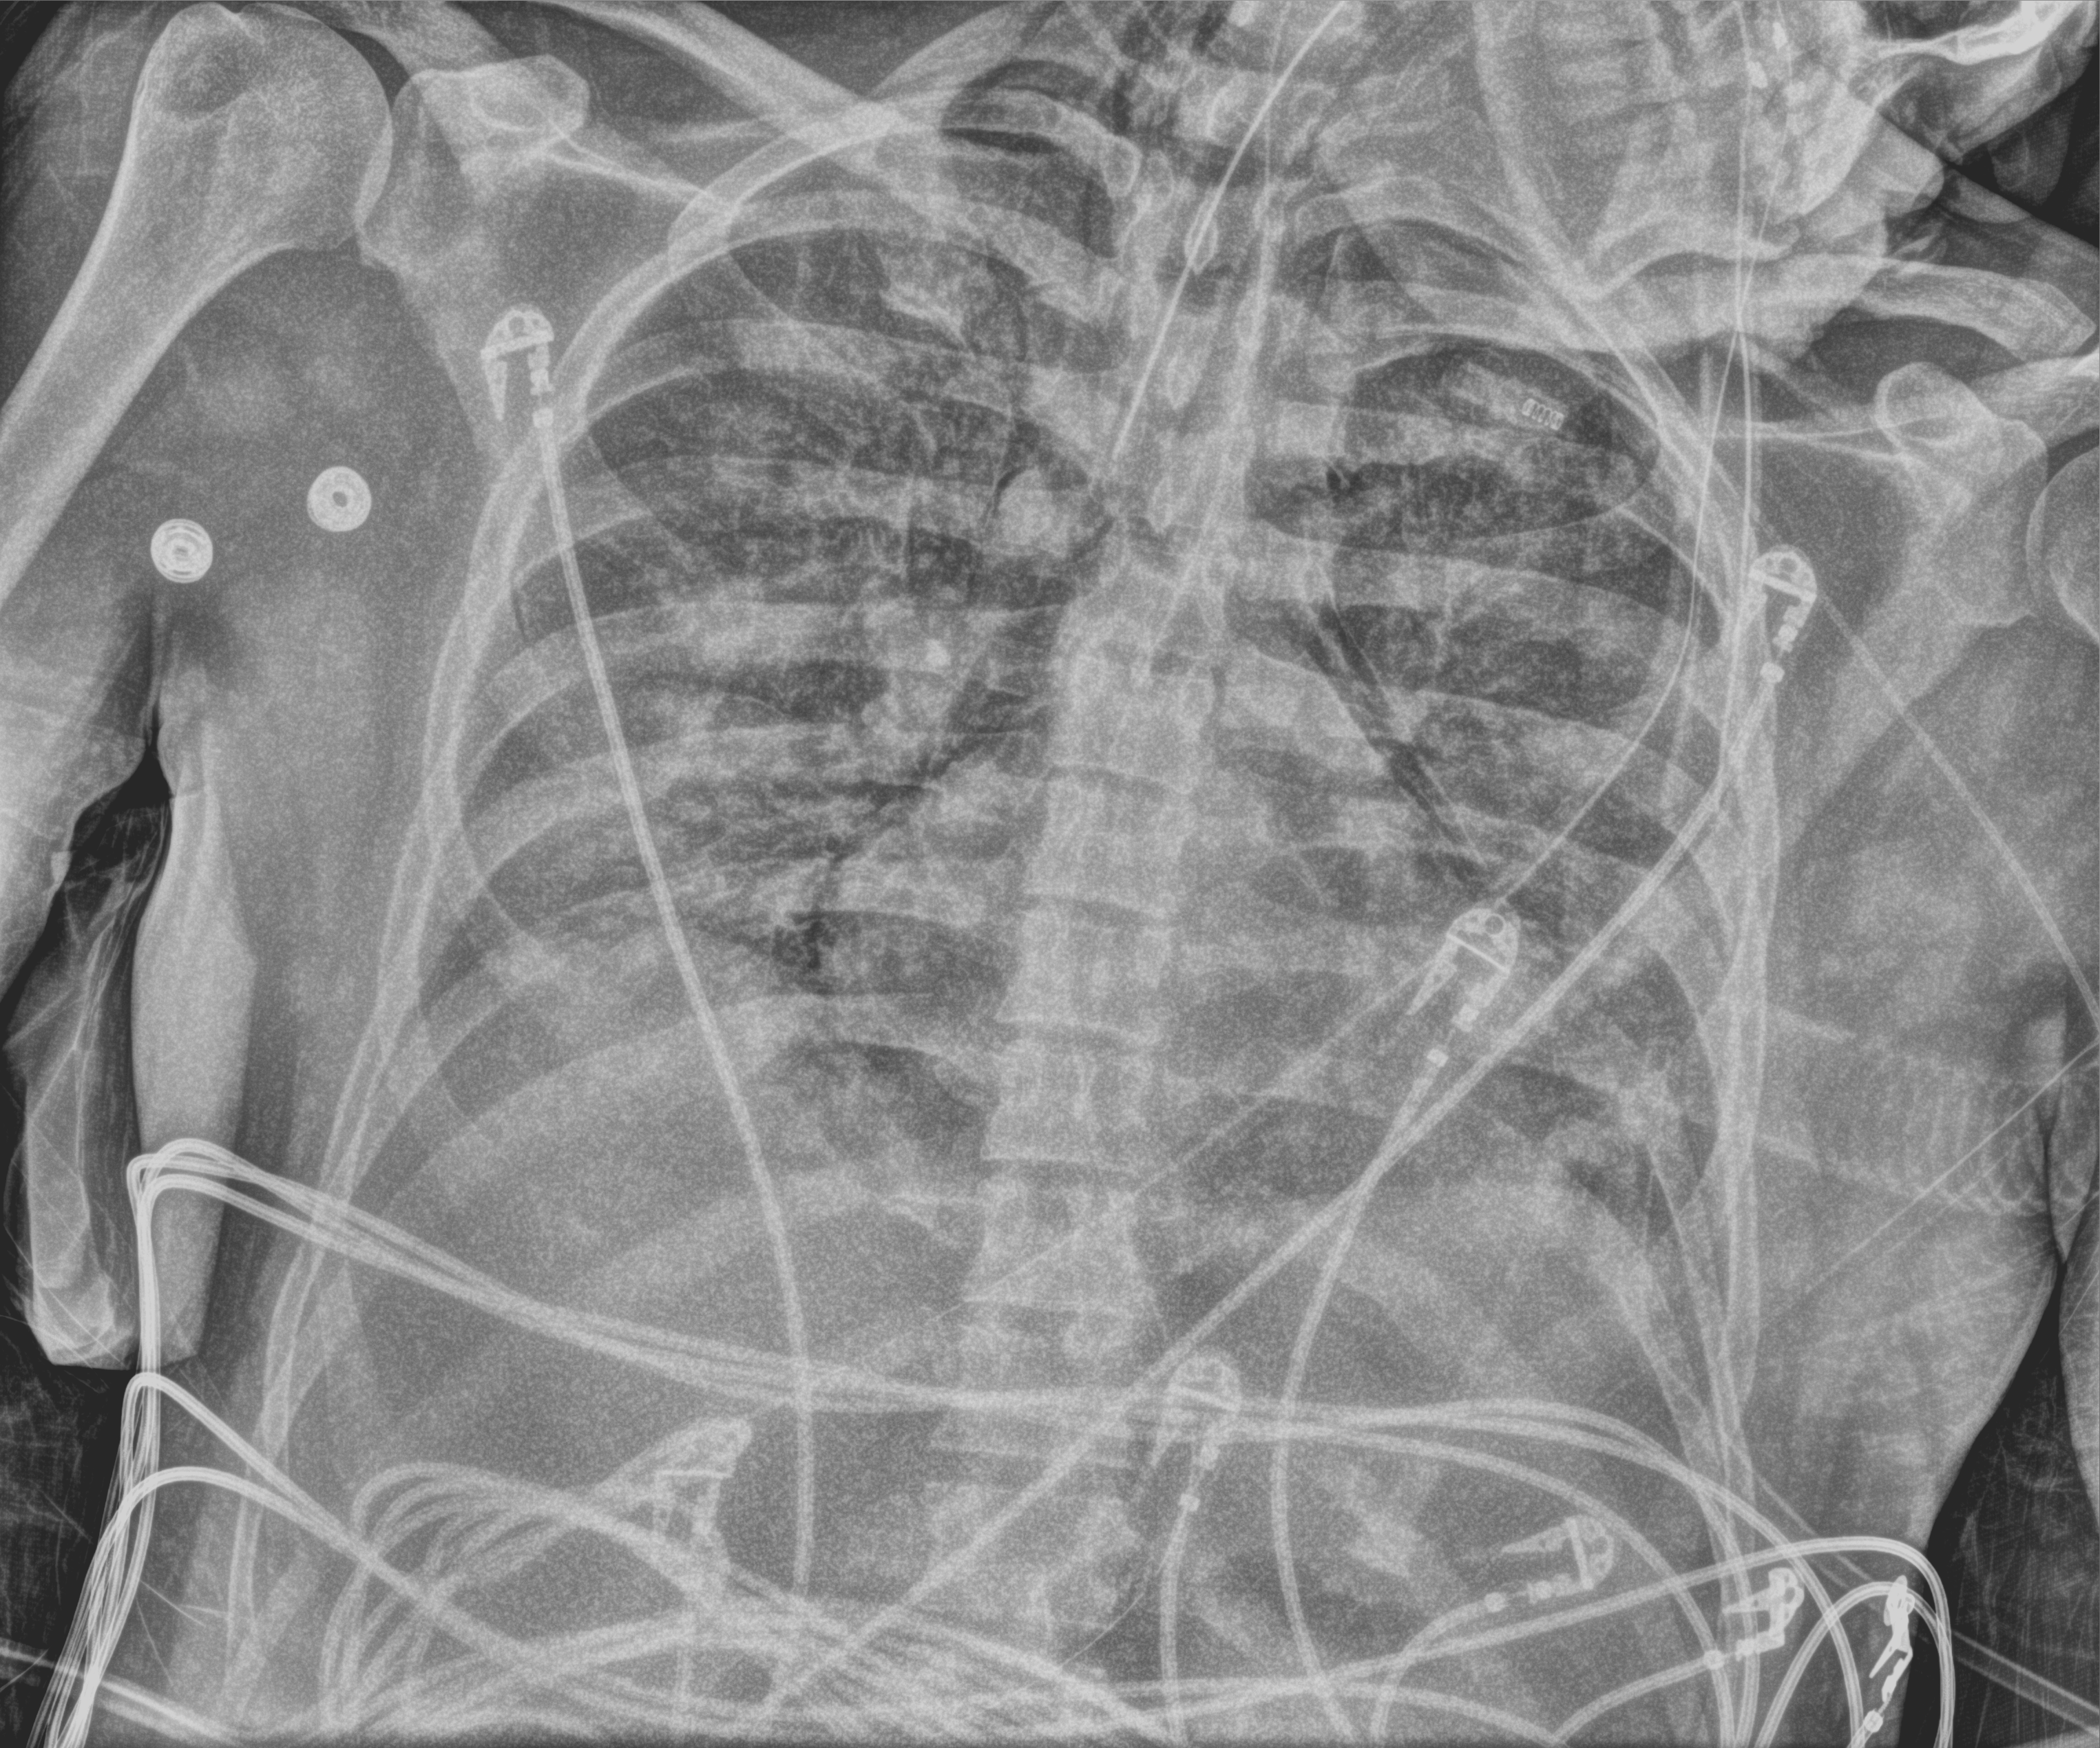
Portable chest radiograph; anteroposterior (AP) projection. Male patient hospitalised with COVID-19, age 18–59 years.
Hospital-stay facts (about this admission, not read from this image; timing relative to this image not recorded):
- admitted to intensive care during this hospital stay: yes